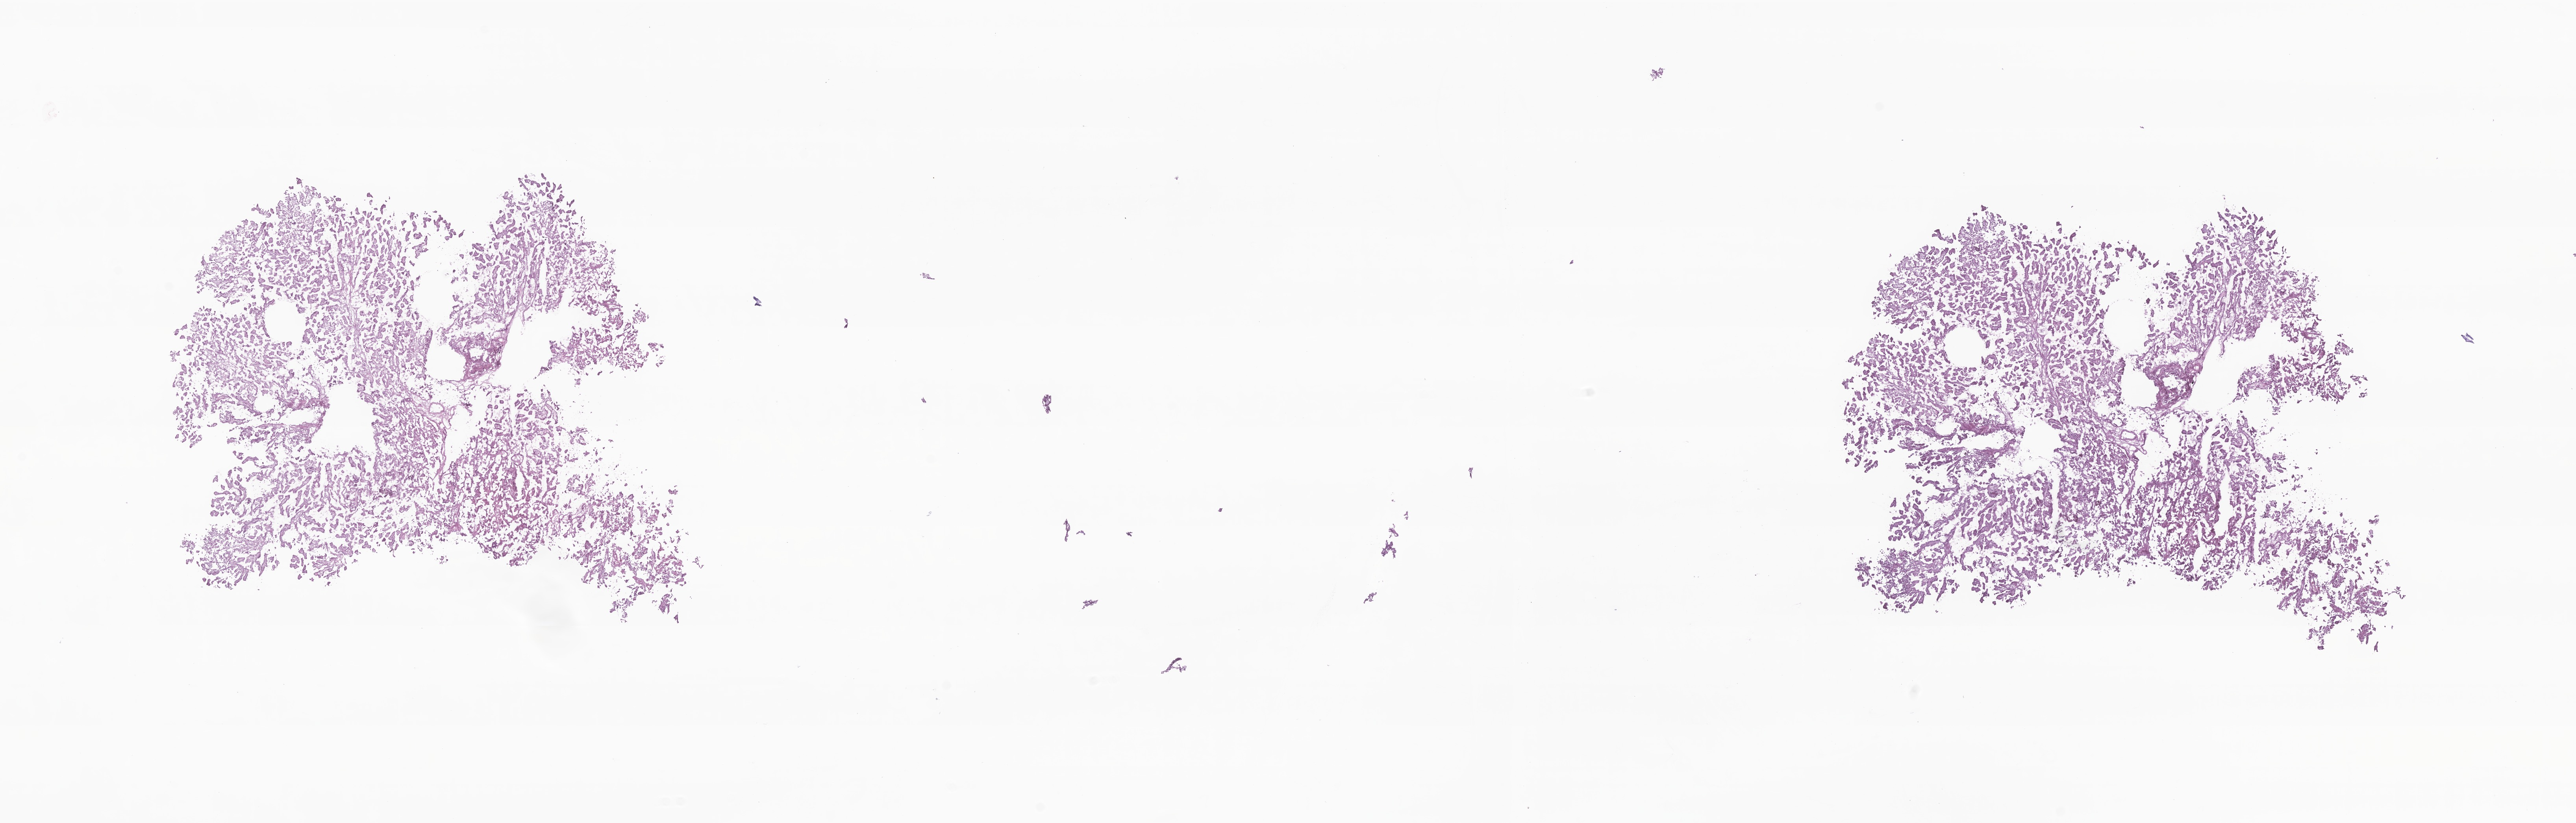
Whole-slide image, haematoxylin and eosin stain of tumor tissue from the brain — a low-resolution overview of the entire scanned area, about 27.6 x 8.8 mm. Frozen section (OCT-embedded). Patient female; age 231 months.
- diagnosis (ICD-O-3 morphology term): Choroid plexus papilloma, NOS